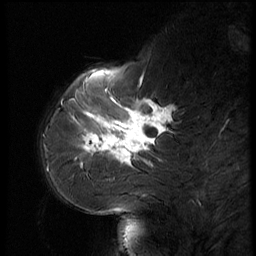
Breast MRI (dynamic contrast-enhanced), one sagittal slice. Slice 18 of 56 in the series (ordered by position). Dynamic contrast-enhanced series, image 2 of 3 at this slice position (ordered by acquisition). 1.5 T. TE 4.2 ms, TR 9 ms. 256 × 256 image matrix, field of view 180 × 180 mm. Female patient, age 61 years. From the clinical record (not read from this slice): setting: breast cancer imaged before/during neoadjuvant chemotherapy; receptor status: HR-positive, HER2-negative.
Structures marked on this image (semi-automatically segmented with operator editing):
- analysis volume of interest (the breast-tissue region the enhancement analysis was run in; not a lesion): bounding box <65,74,185,175> (left, top, right, bottom; pixels)
- tumour enhancement mask (voxels above the 140 % enhancement threshold inside the analysis volume of interest): <82,98,173,168>